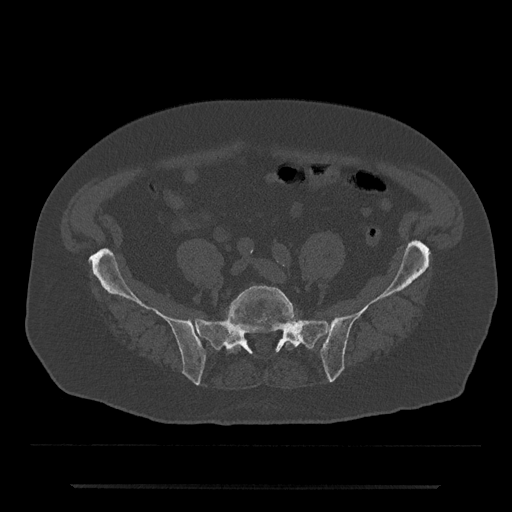
CT including the spine, one axial slice; slice 257 of 797 in the series (ordered by position); reconstruction kernel Br40s/3; bone window (W 1800 / L 400 HU); 512 × 512 image matrix, field of view 434 × 434 mm. Male patient, age 80 years. From the clinical record (not read from this slice): primary cancer: prostate.
Structures marked on this image (semi-automatic segmentation, software-assisted and operator-edited):
- L5 vertebra: bounding box (x1, y1, x2, y2) in pixels: (226, 286, 298, 353)